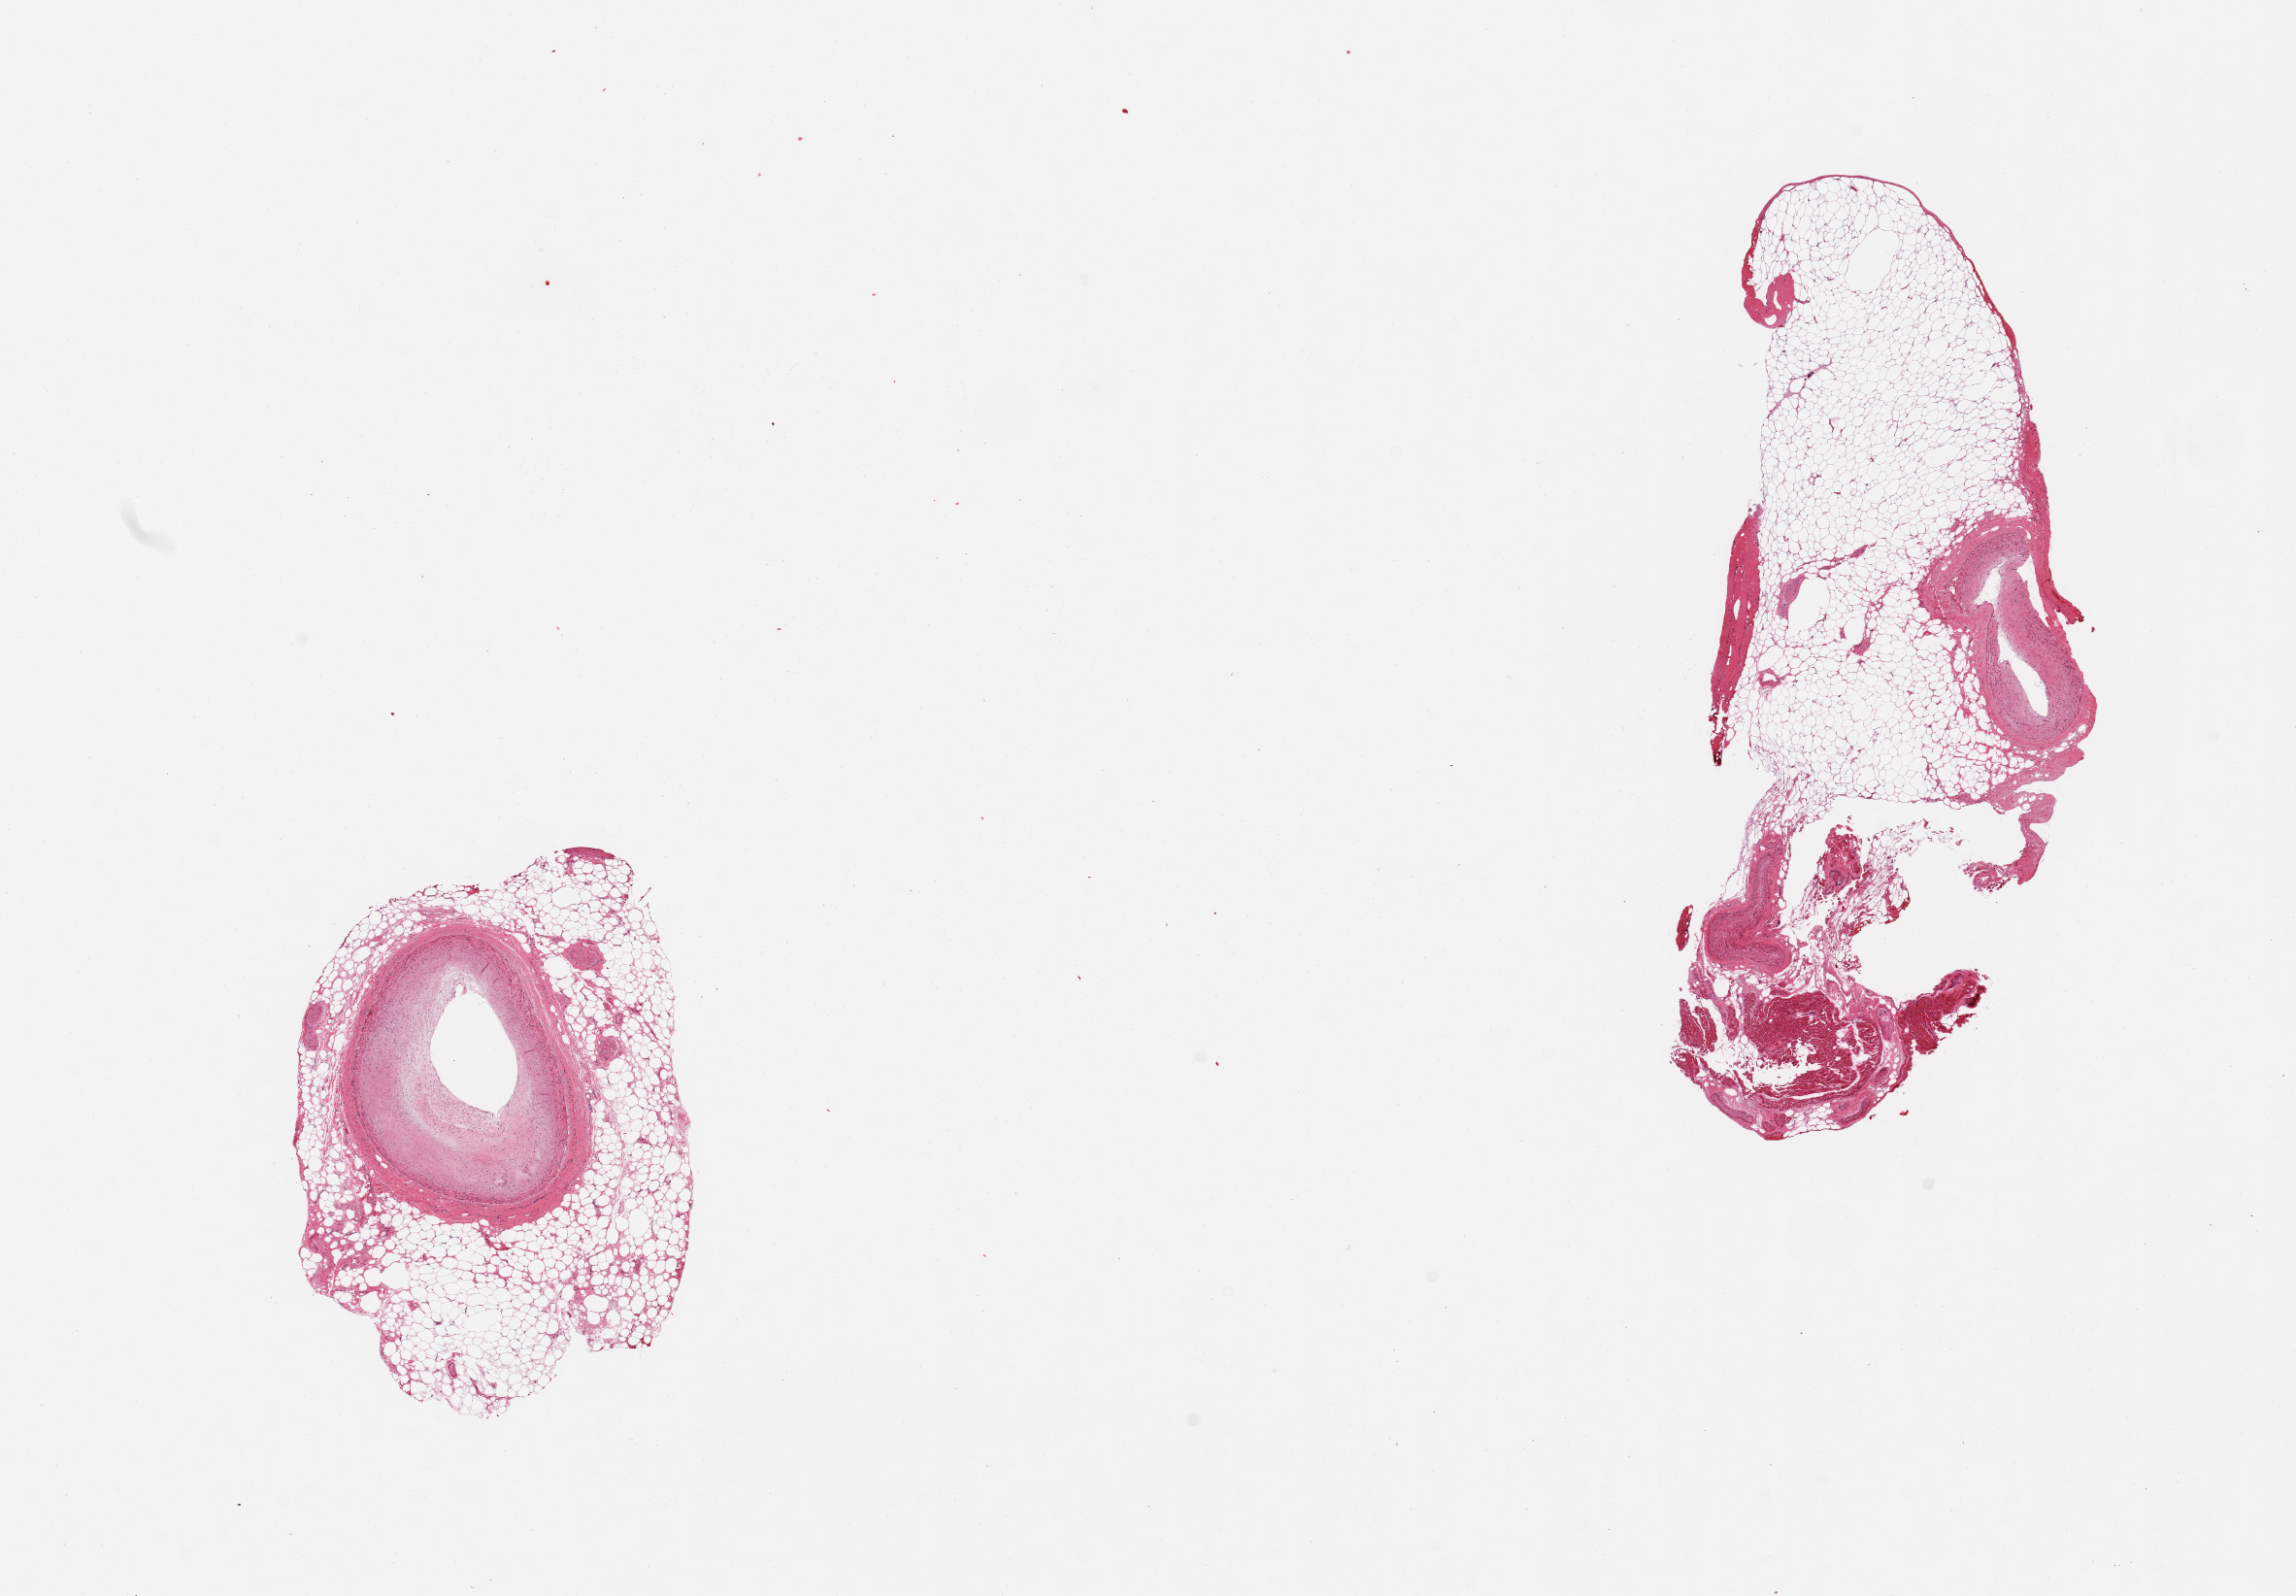
Digitized H&E-stained section, shown as a low-resolution overview of the whole scanned area (about 18.7 x 13.0 mm, acquisition: 20x scan). PAXgene-fixed paraffin-embedded (PFPE) section. Target tissue: coronary artery. Donor tissue sample. Donor sex: male.
Reviewer comment on this tissue sample: 2 pieces, minimal target artery with ~60-70% occlusive atherosis, mainly epicaridal fat.